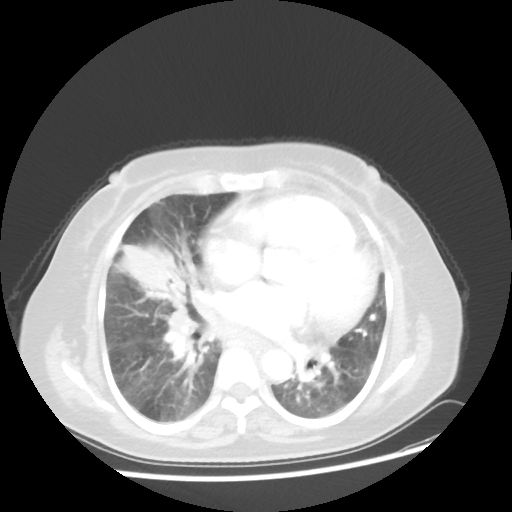
Chest CT, one axial slice; slice 21 of 45 in the series (ordered by position); reconstruction kernel STANDARD; 100 kVp; lung window (W 1500 / L -600 HU); 512 × 512 image matrix, field of view 359 × 359 mm. Female patient, age 67 years. From the clinical record (not read from this slice): clinical TNM (as recorded): T2a N3 M1a.
Outlined on this slice (bounding box drawn by a radiologist):
- lung tumour (recorded histology: adenocarcinoma): bounding box <122,242,187,303> (left, top, right, bottom; pixels)